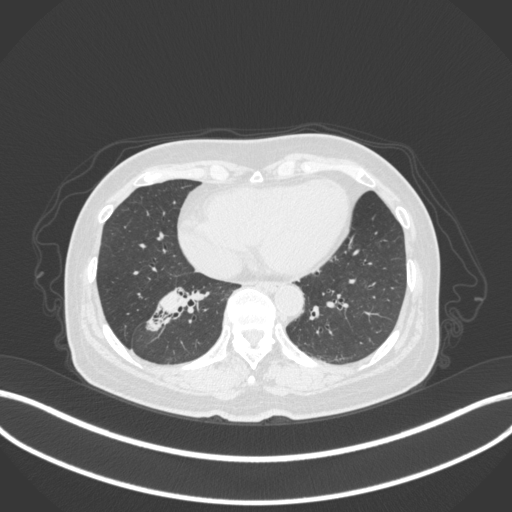
Chest CT, one axial slice; slice 137 of 429 in the series (ordered by position); 120 kVp; lung window (W 1500 / L -600 HU); 1 mm slice thickness; 512 × 512 image matrix, field of view 400 × 400 mm. Patient: female, 67 years. Case-level facts recorded for this patient, not image findings: clinical TNM (as recorded): T1c N1 M0; histopathological grade: G2-3.
Outlined on this slice (bounding box drawn by a radiologist):
- lung tumour (recorded histology: adenocarcinoma): box from (x=141, y=280) to (x=211, y=333) px